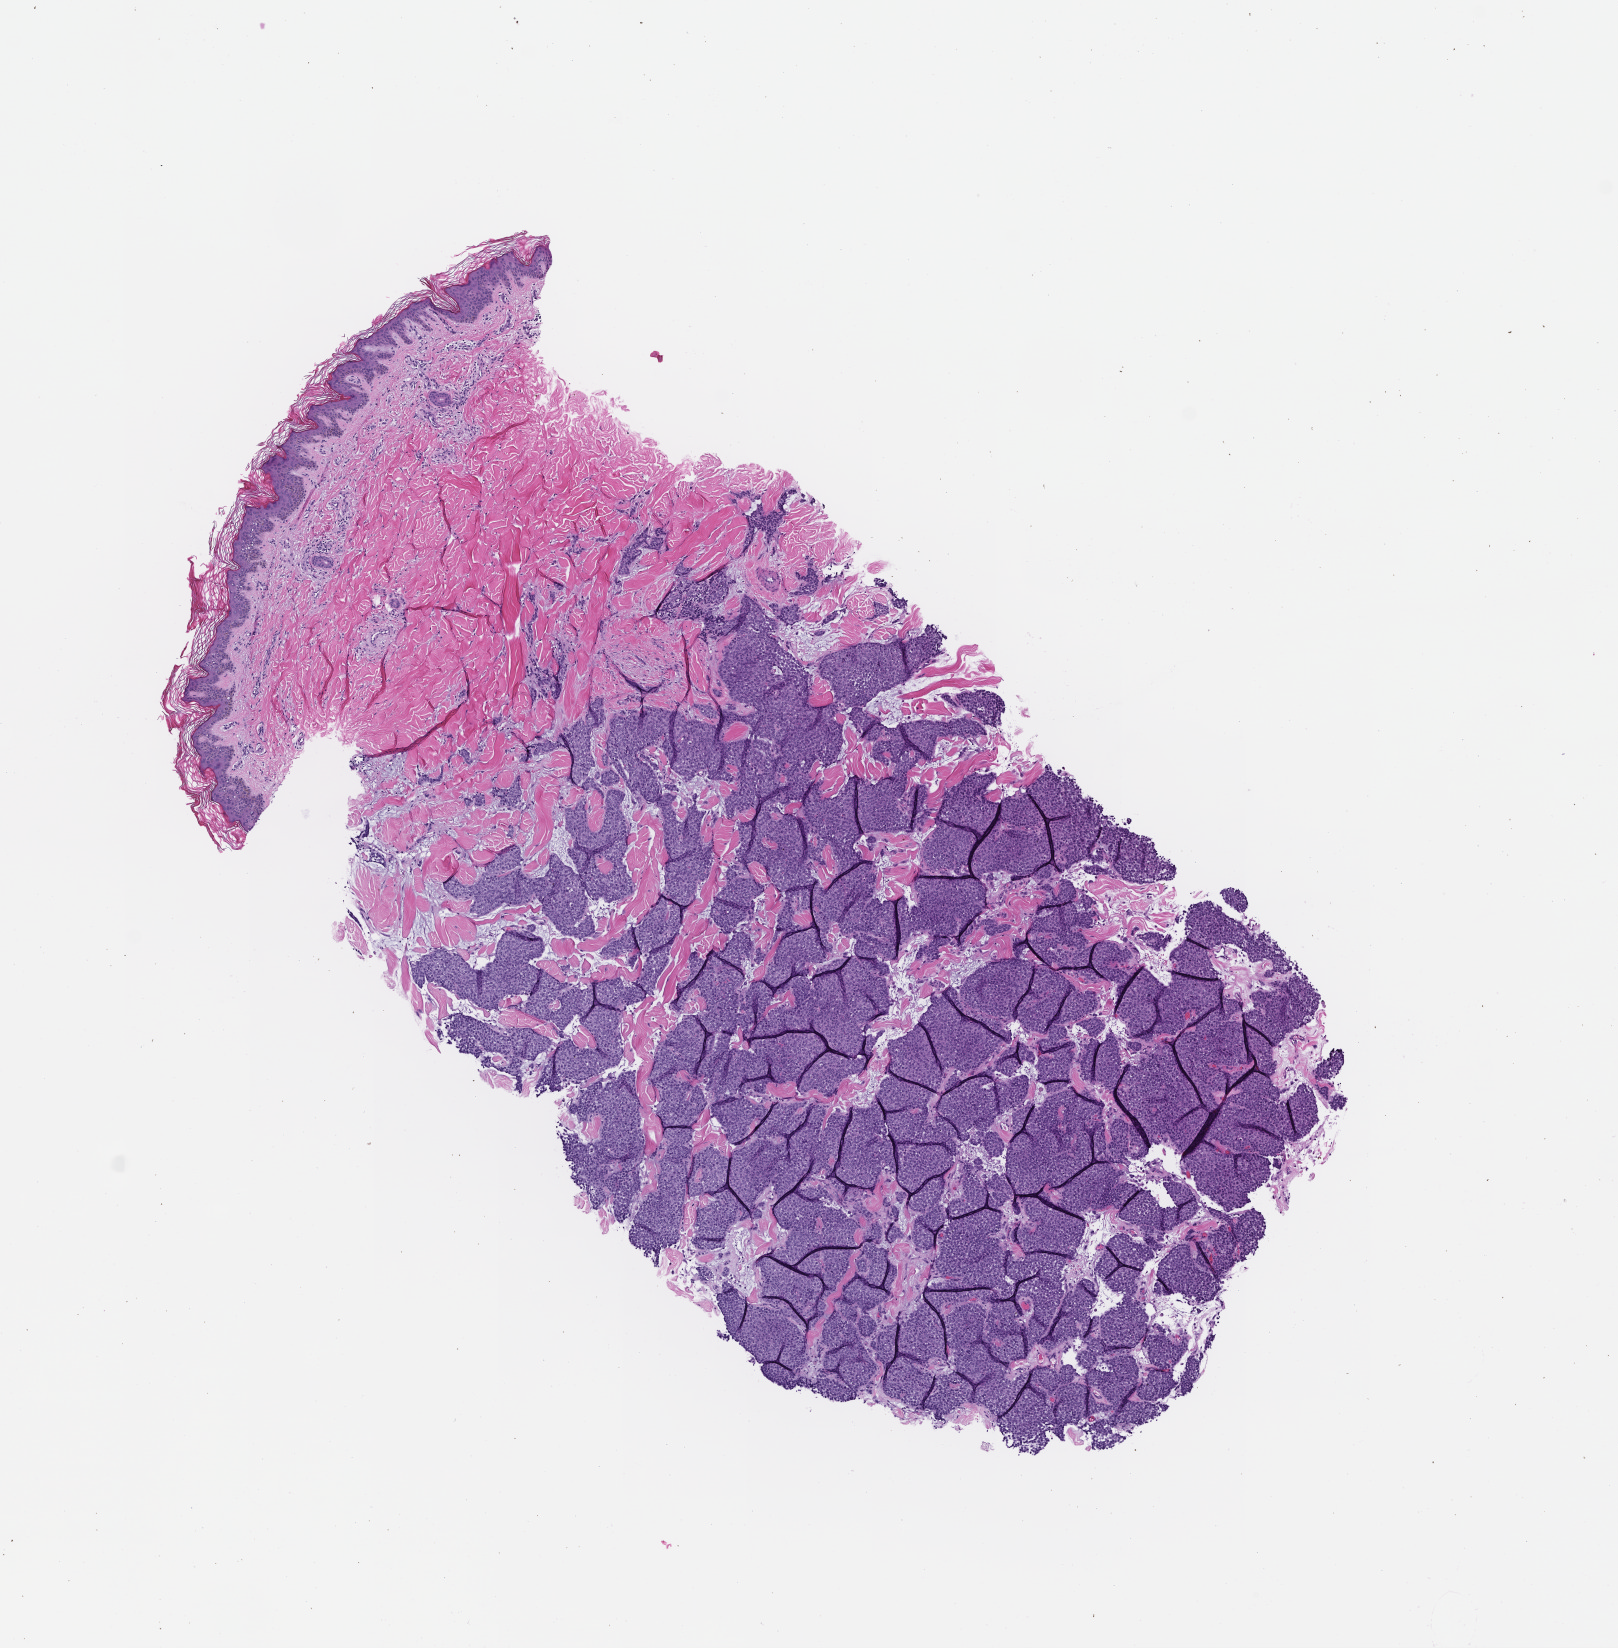
Digitized hematoxylin and eosin (H&E)-stained section, low-resolution overview of the scanned area, about 6.5 x 6.7 mm, formalin-fixed, paraffin-embedded (FFPE) tissue, specimen time point: collected at baseline (before treatment). Patient: male.
This section: metastasis (sampled organ not recorded). Primary diagnosis of the patient: Non-Small Cell Lung Carcinoma.